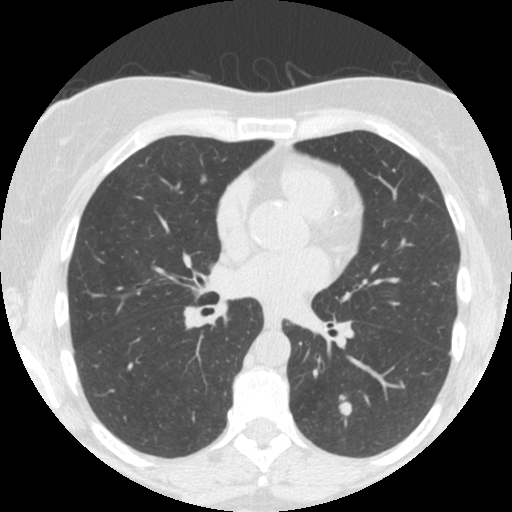
Low-dose screening chest CT, one axial slice; position 78 of 150 along the scan axis; 120 kVp; lung window (W 1500 / L -600 HU); 2.5 mm slice thickness; 512 × 512 image matrix, field of view 300 × 300 mm.
Structures marked on this image (manually delineated by an expert):
- lesion 1 (tumor, lower lobe of left lung): box from (x=339, y=395) to (x=352, y=421) px